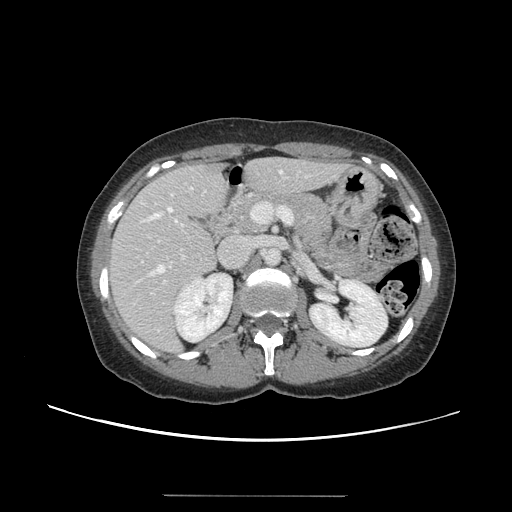
Contrast-enhanced abdominal CT, one axial slice; slice 74 of 144 in the series (ordered by position); 120 kVp; intravenous contrast given; soft-tissue window (W 400 / L 40 HU); 2.5 mm slice thickness; 512 × 512 image matrix, field of view 380 × 380 mm. Female patient, age 53 years. Case-level facts recorded for this patient, not image findings: diagnosis: colorectal cancer liver metastases, imaged before liver resection; multiple liver metastases: yes; largest metastasis: 1.1 cm; chemotherapy before resection: no.
Annotated regions visible in this slice (manually delineated by an expert):
- hepatic veins: box from (x=150, y=170) to (x=282, y=275) px
- liver: (x=109, y=159)–(x=342, y=352)
- planned liver remnant (the part of the liver to remain after resection): (x=110, y=159)–(x=320, y=300)
- portal vein (with intrahepatic branches): (x=141, y=203)–(x=294, y=294)